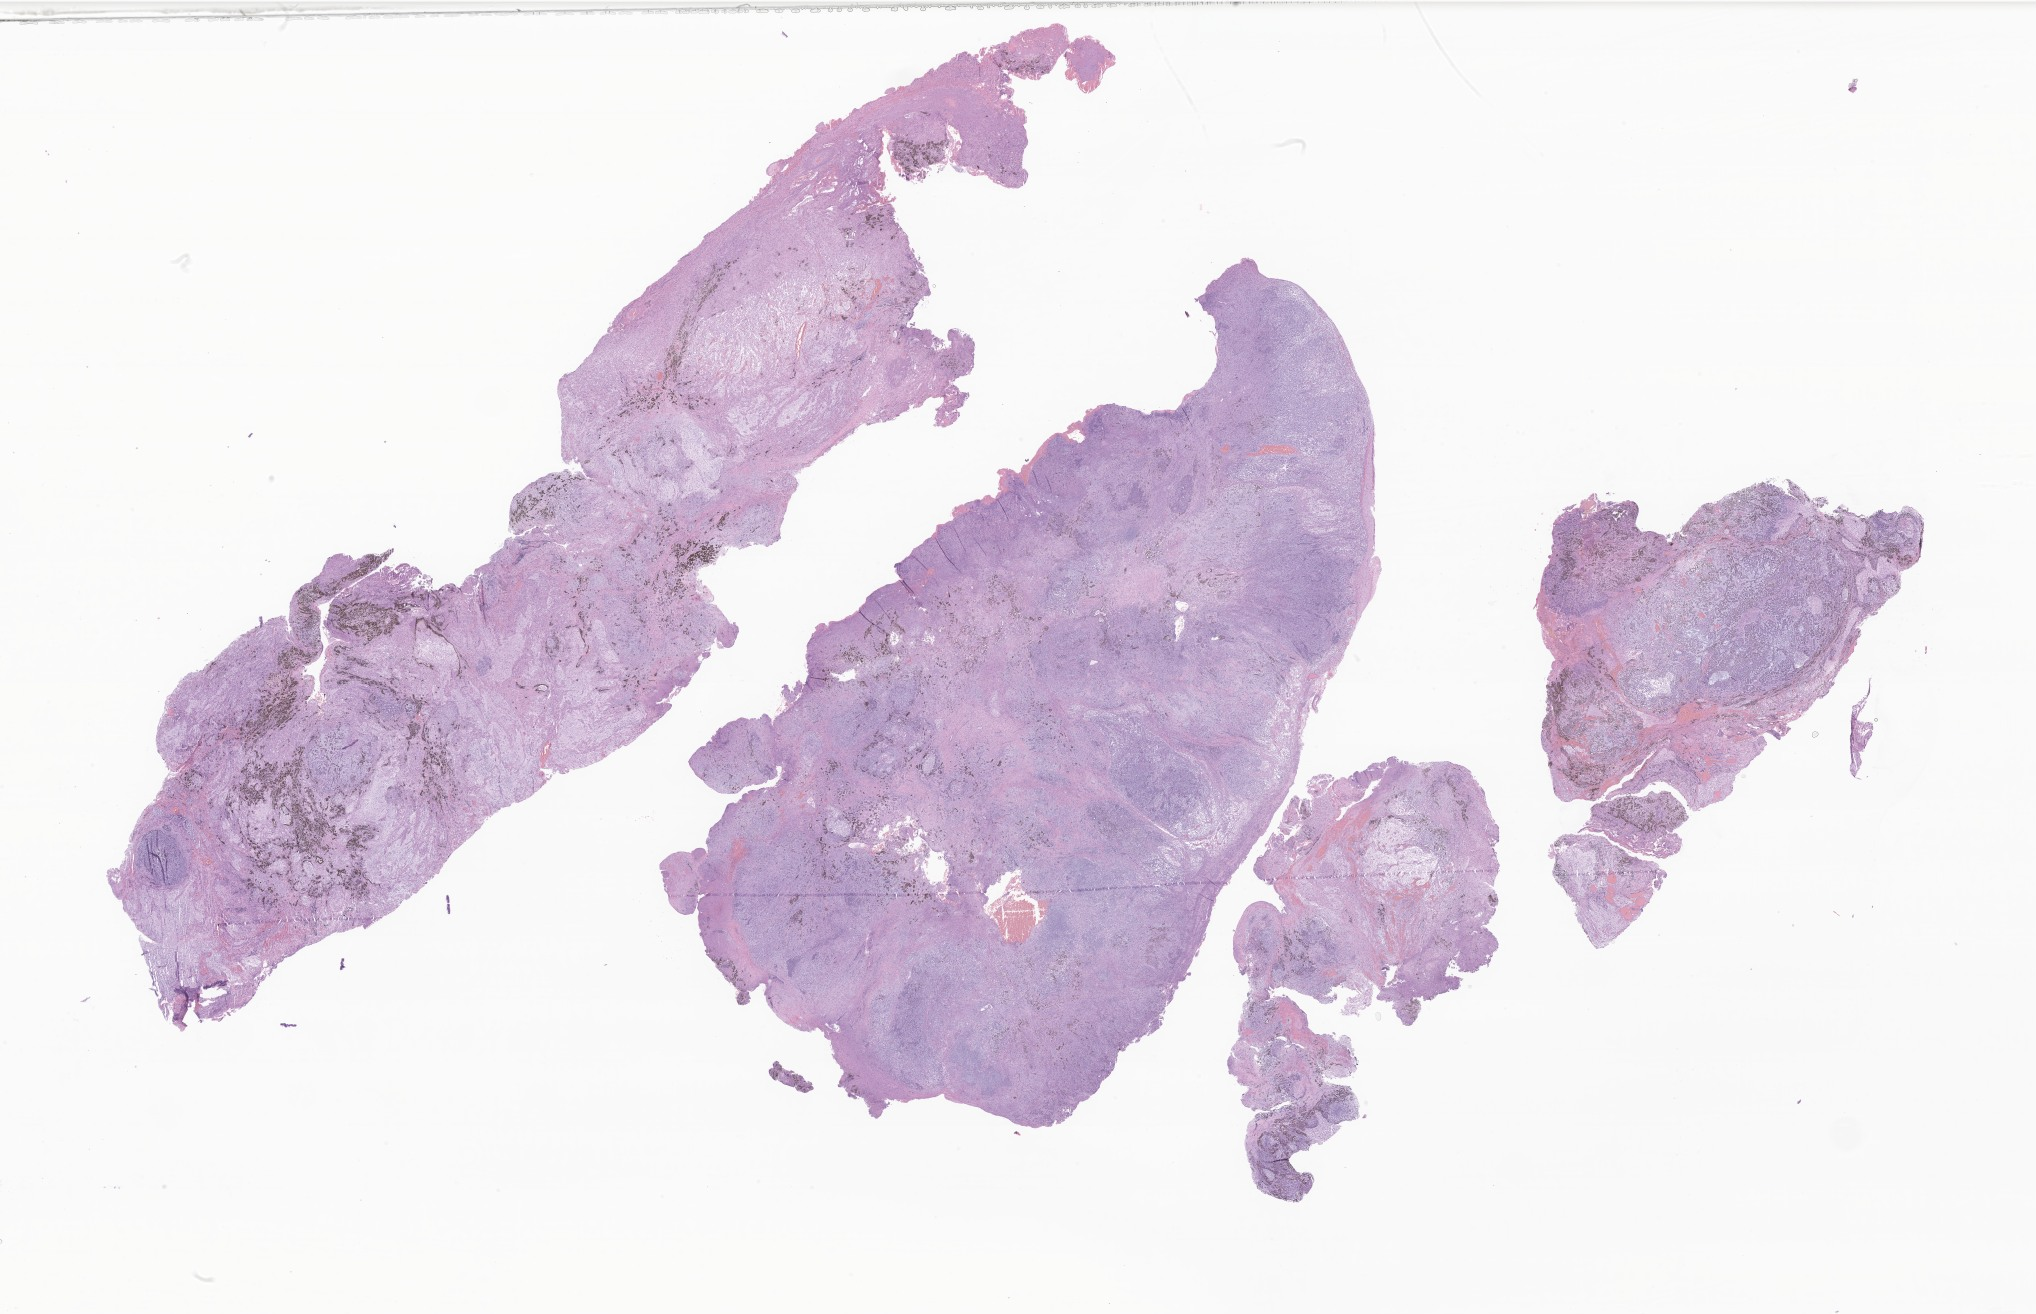
Whole-slide image, hematoxylin and eosin (H&E) stain of tumor tissue from the brain, shown as a low-resolution overview of the whole scanned area (about 34.3 x 22.2 mm), formalin-fixed, paraffin-embedded (FFPE) tissue. Patient: male, age 111 days.
Diagnosis: Pineoblastoma.